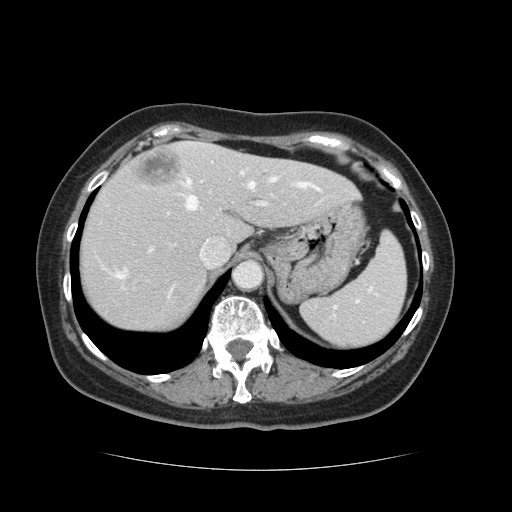
Contrast-enhanced abdominal CT, one axial slice. 120 kVp. Intravenous contrast given. Soft-tissue window (W 400 / L 40 HU). 2.5 mm slice thickness. 512 × 512 image matrix, field of view 366 × 366 mm. Female patient, age 67 years. From the clinical record (not read from this slice): diagnosis: colorectal cancer liver metastases, imaged before liver resection; multiple liver metastases: yes; largest metastasis: 3 cm; disease in both lobes: yes.
Structures marked on this image (manually delineated by an expert):
- hepatic veins: bounding box <118,171,317,298> (left, top, right, bottom; pixels)
- liver: <79,143,357,332>
- planned liver remnant (the part of the liver to remain after resection): <79,154,357,332>
- portal vein (with intrahepatic branches): <150,160,268,251>
- liver metastasis: <135,153,179,188>